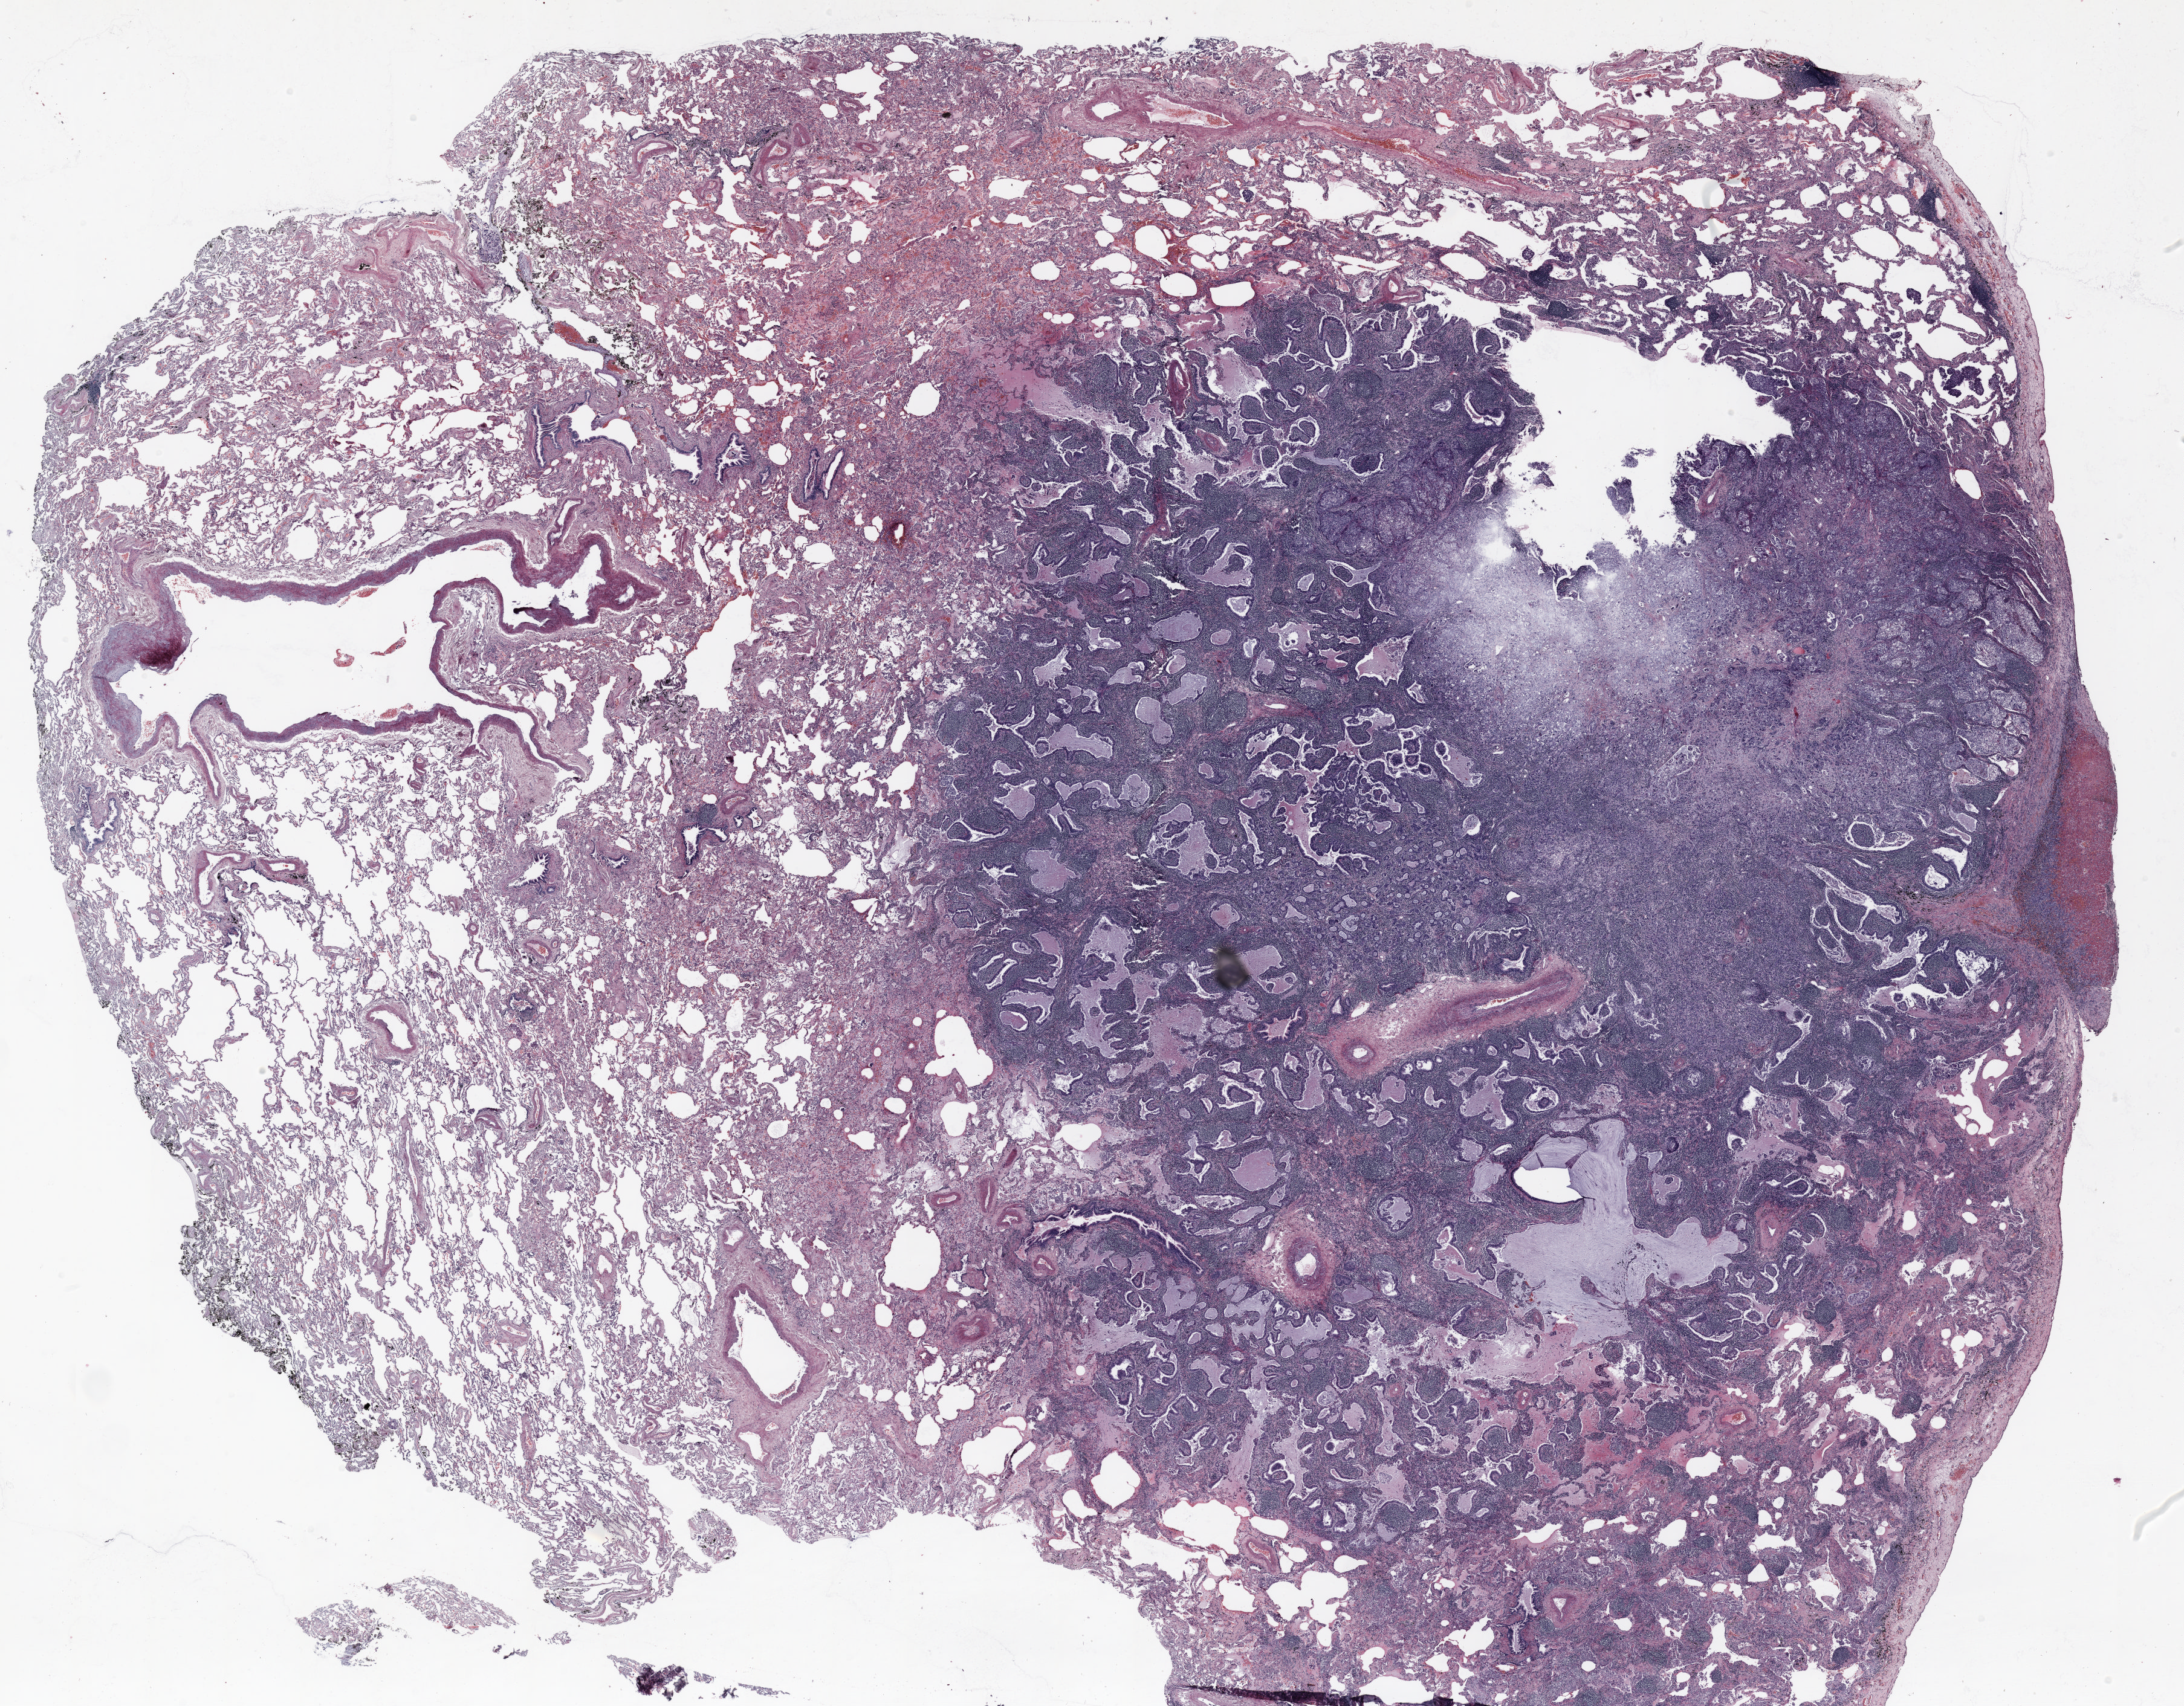
Whole-slide histology image, H&E-stained — low-resolution overview of the scanned area, about 29.0 x 22.7 mm (from a 20x scan); formalin-fixed paraffin-embedded (FFPE) section; lung. Male patient, aged 71 at enrolment. Former smoker at enrolment.
Participant's lung-cancer diagnosis: Adenocarcinoma, NOS.